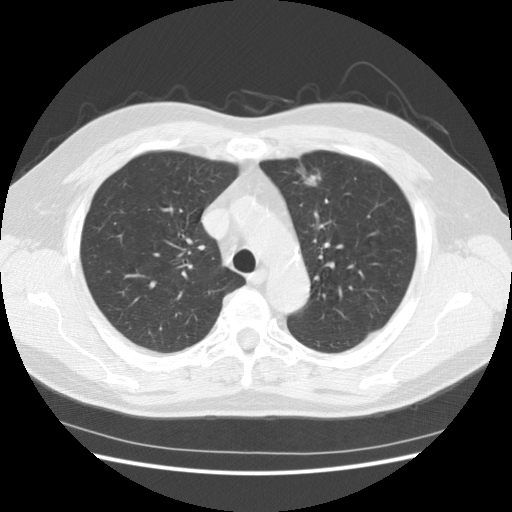
Chest CT (low-dose screening protocol), one axial image; baseline annual screen; lung window (W 1500 / L -600 HU); 2.5 mm slice thickness; 120 kVp; slice 43 of 151 in the series. Male participant, aged 63 years at enrolment. Former smoker at enrolment.
Expert-annotated lung lesion, bounding box <282,154,337,204> (left, top, right, bottom; pixels). Reader record for this screening exam (exam-level; its link to the box is not recorded): non-calcified nodule or mass ≥4 mm, lingula, 18 × 9 mm, poorly defined margins, soft tissue attenuation. Participant outcome: lung cancer diagnosed 475 days after this screen — adenocarcinoma, NOS, left upper lobe, moderately differentiated (G2), stage IA (AJCC 6th edition), 14 mm at pathology.